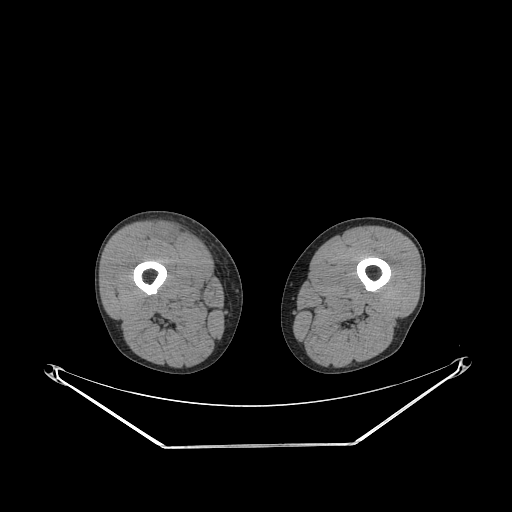
CT of an extremity soft-tissue mass (from a PET/CT study), one axial slice; slice 236 of 311 in the series (ordered by position); soft-tissue window (W 400 / L 40 HU); 3.75 mm slice thickness; 512 × 512 image matrix, field of view 500 × 500 mm. Male patient. From the clinical record (not read from this slice): histological type: pleiomorphic leiomyosarcoma; grade: intermediate; site of the primary tumour: right thigh.
Outlined on this slice (expert contour drawn on MRI and transferred to this co-registered scan by the dataset authors):
- gross tumour volume including surrounding oedema: bounding box <155,224,181,245> (left, top, right, bottom; pixels)